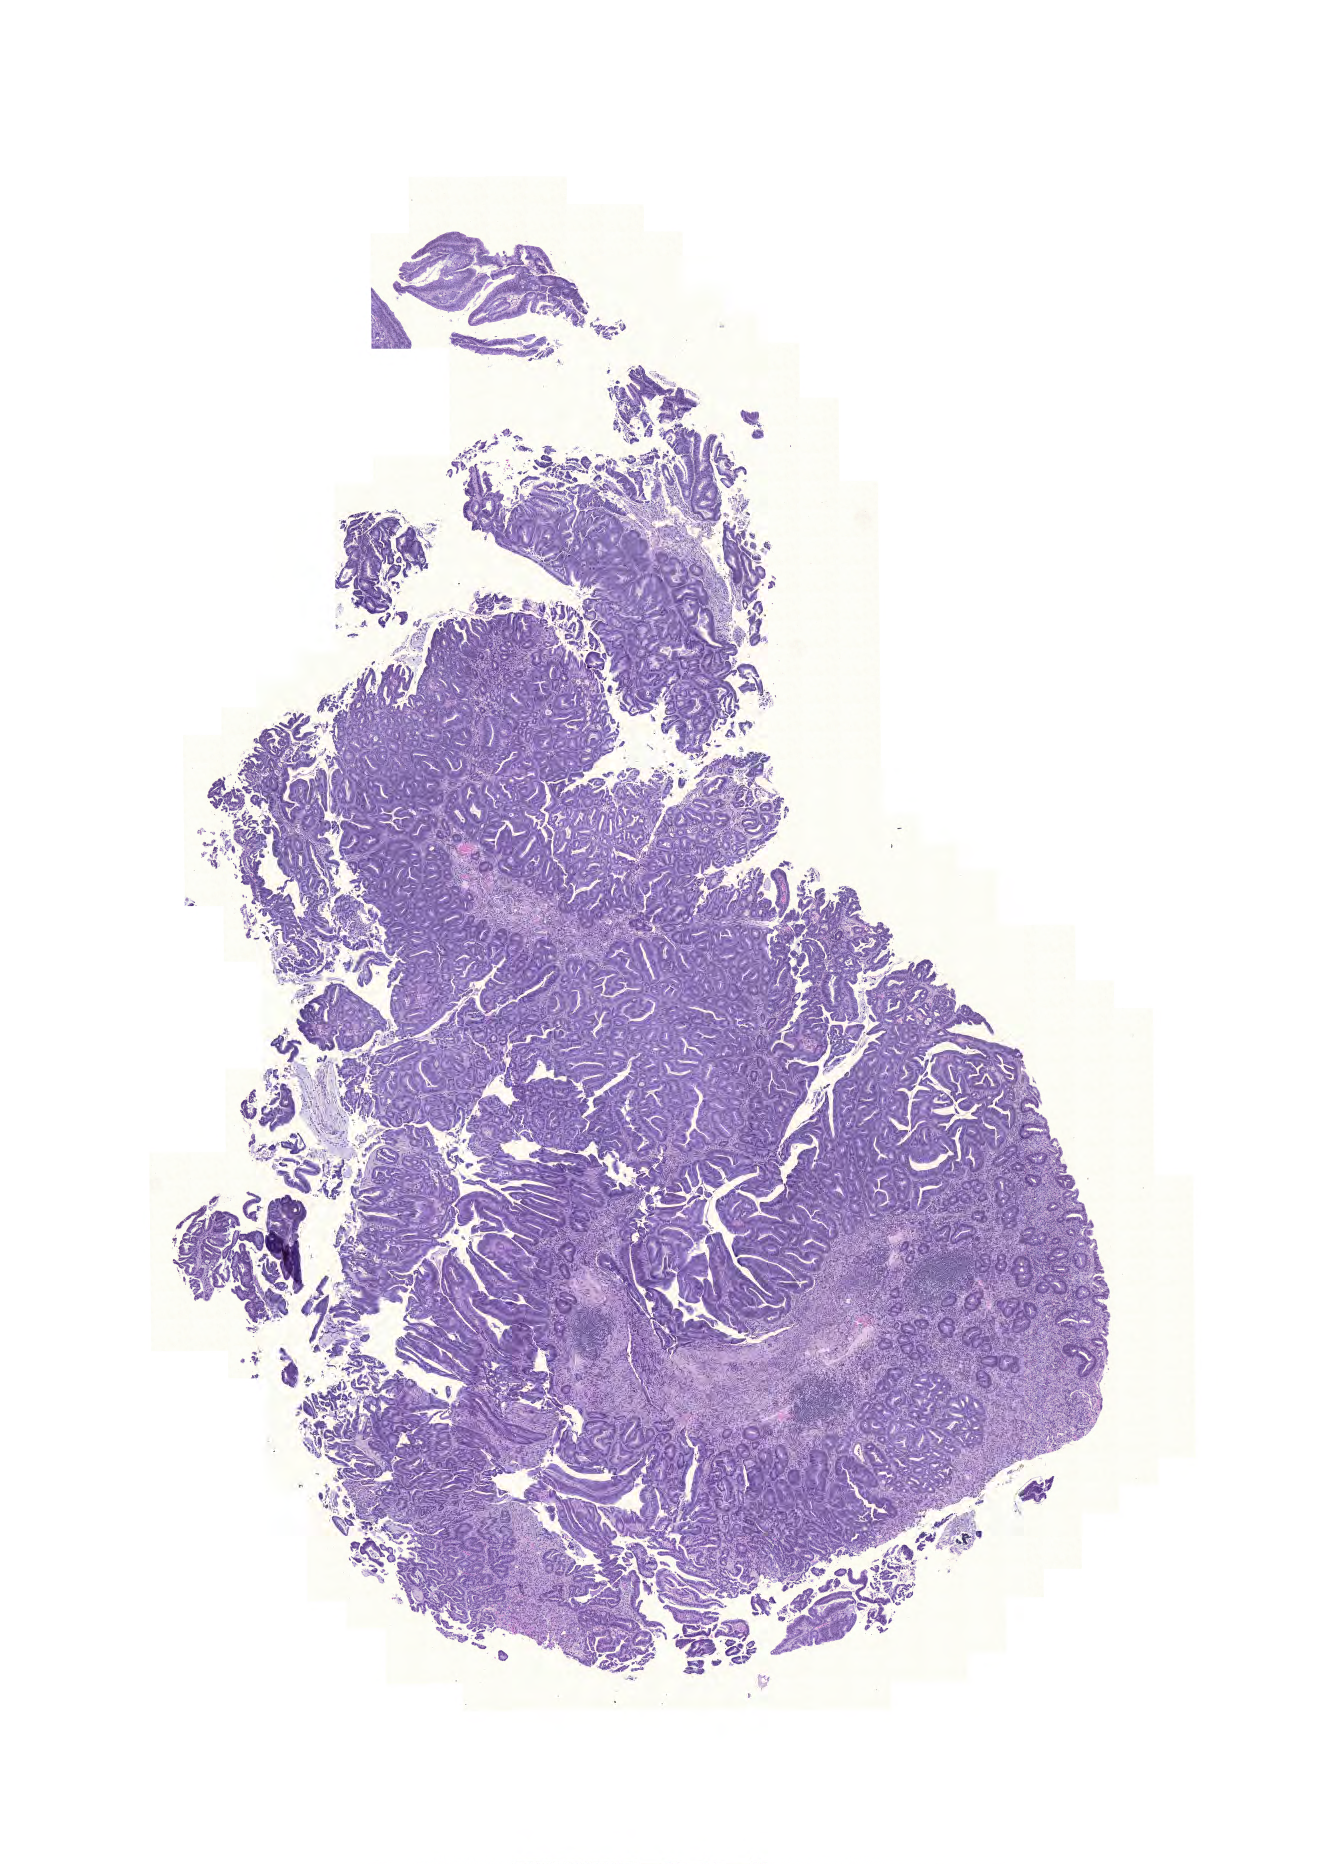
Whole-slide histology image, H&E-stained, low-resolution overview of the scanned area, about 9.8 x 13.9 mm; FFPE section; colon, primary tumour sample. Patient: female, age at initial diagnosis 78 years.
AJCC pathologic stage: IIA (6th edition). Lymph nodes positive (case pathology): 0 of 18 examined. Diagnosis: Adenocarcinoma, NOS.